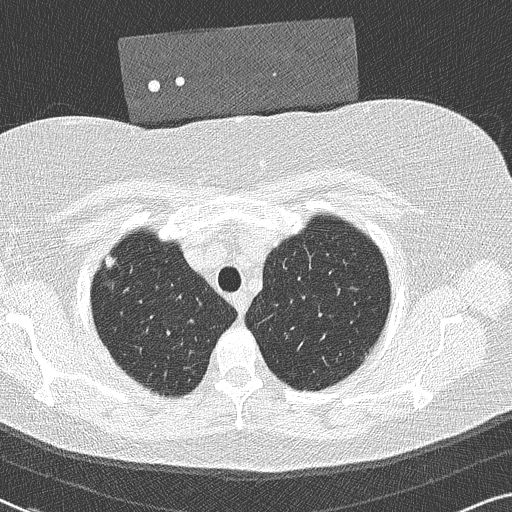
Axial slice from a low-dose chest CT screening exam, baseline annual screen, lung window (W 1500 / L -600 HU), 2 mm slice thickness, slice 39 of 306 in the series. Female, age 58 years at enrolment. Former smoker at enrolment.
Expert-annotated lung lesion, bounding box [x1, y1, x2, y2] px = [93, 248, 131, 294]. No non-calcified nodule or mass ≥4 mm was recorded by the screening reader at this exam. Lung cancer was diagnosed 846 days after this screen: bronchiolo-alveolar adenocarcinoma, NOS, right upper lobe, well differentiated (G1), stage IA (AJCC 6th edition), 9 mm at pathology.